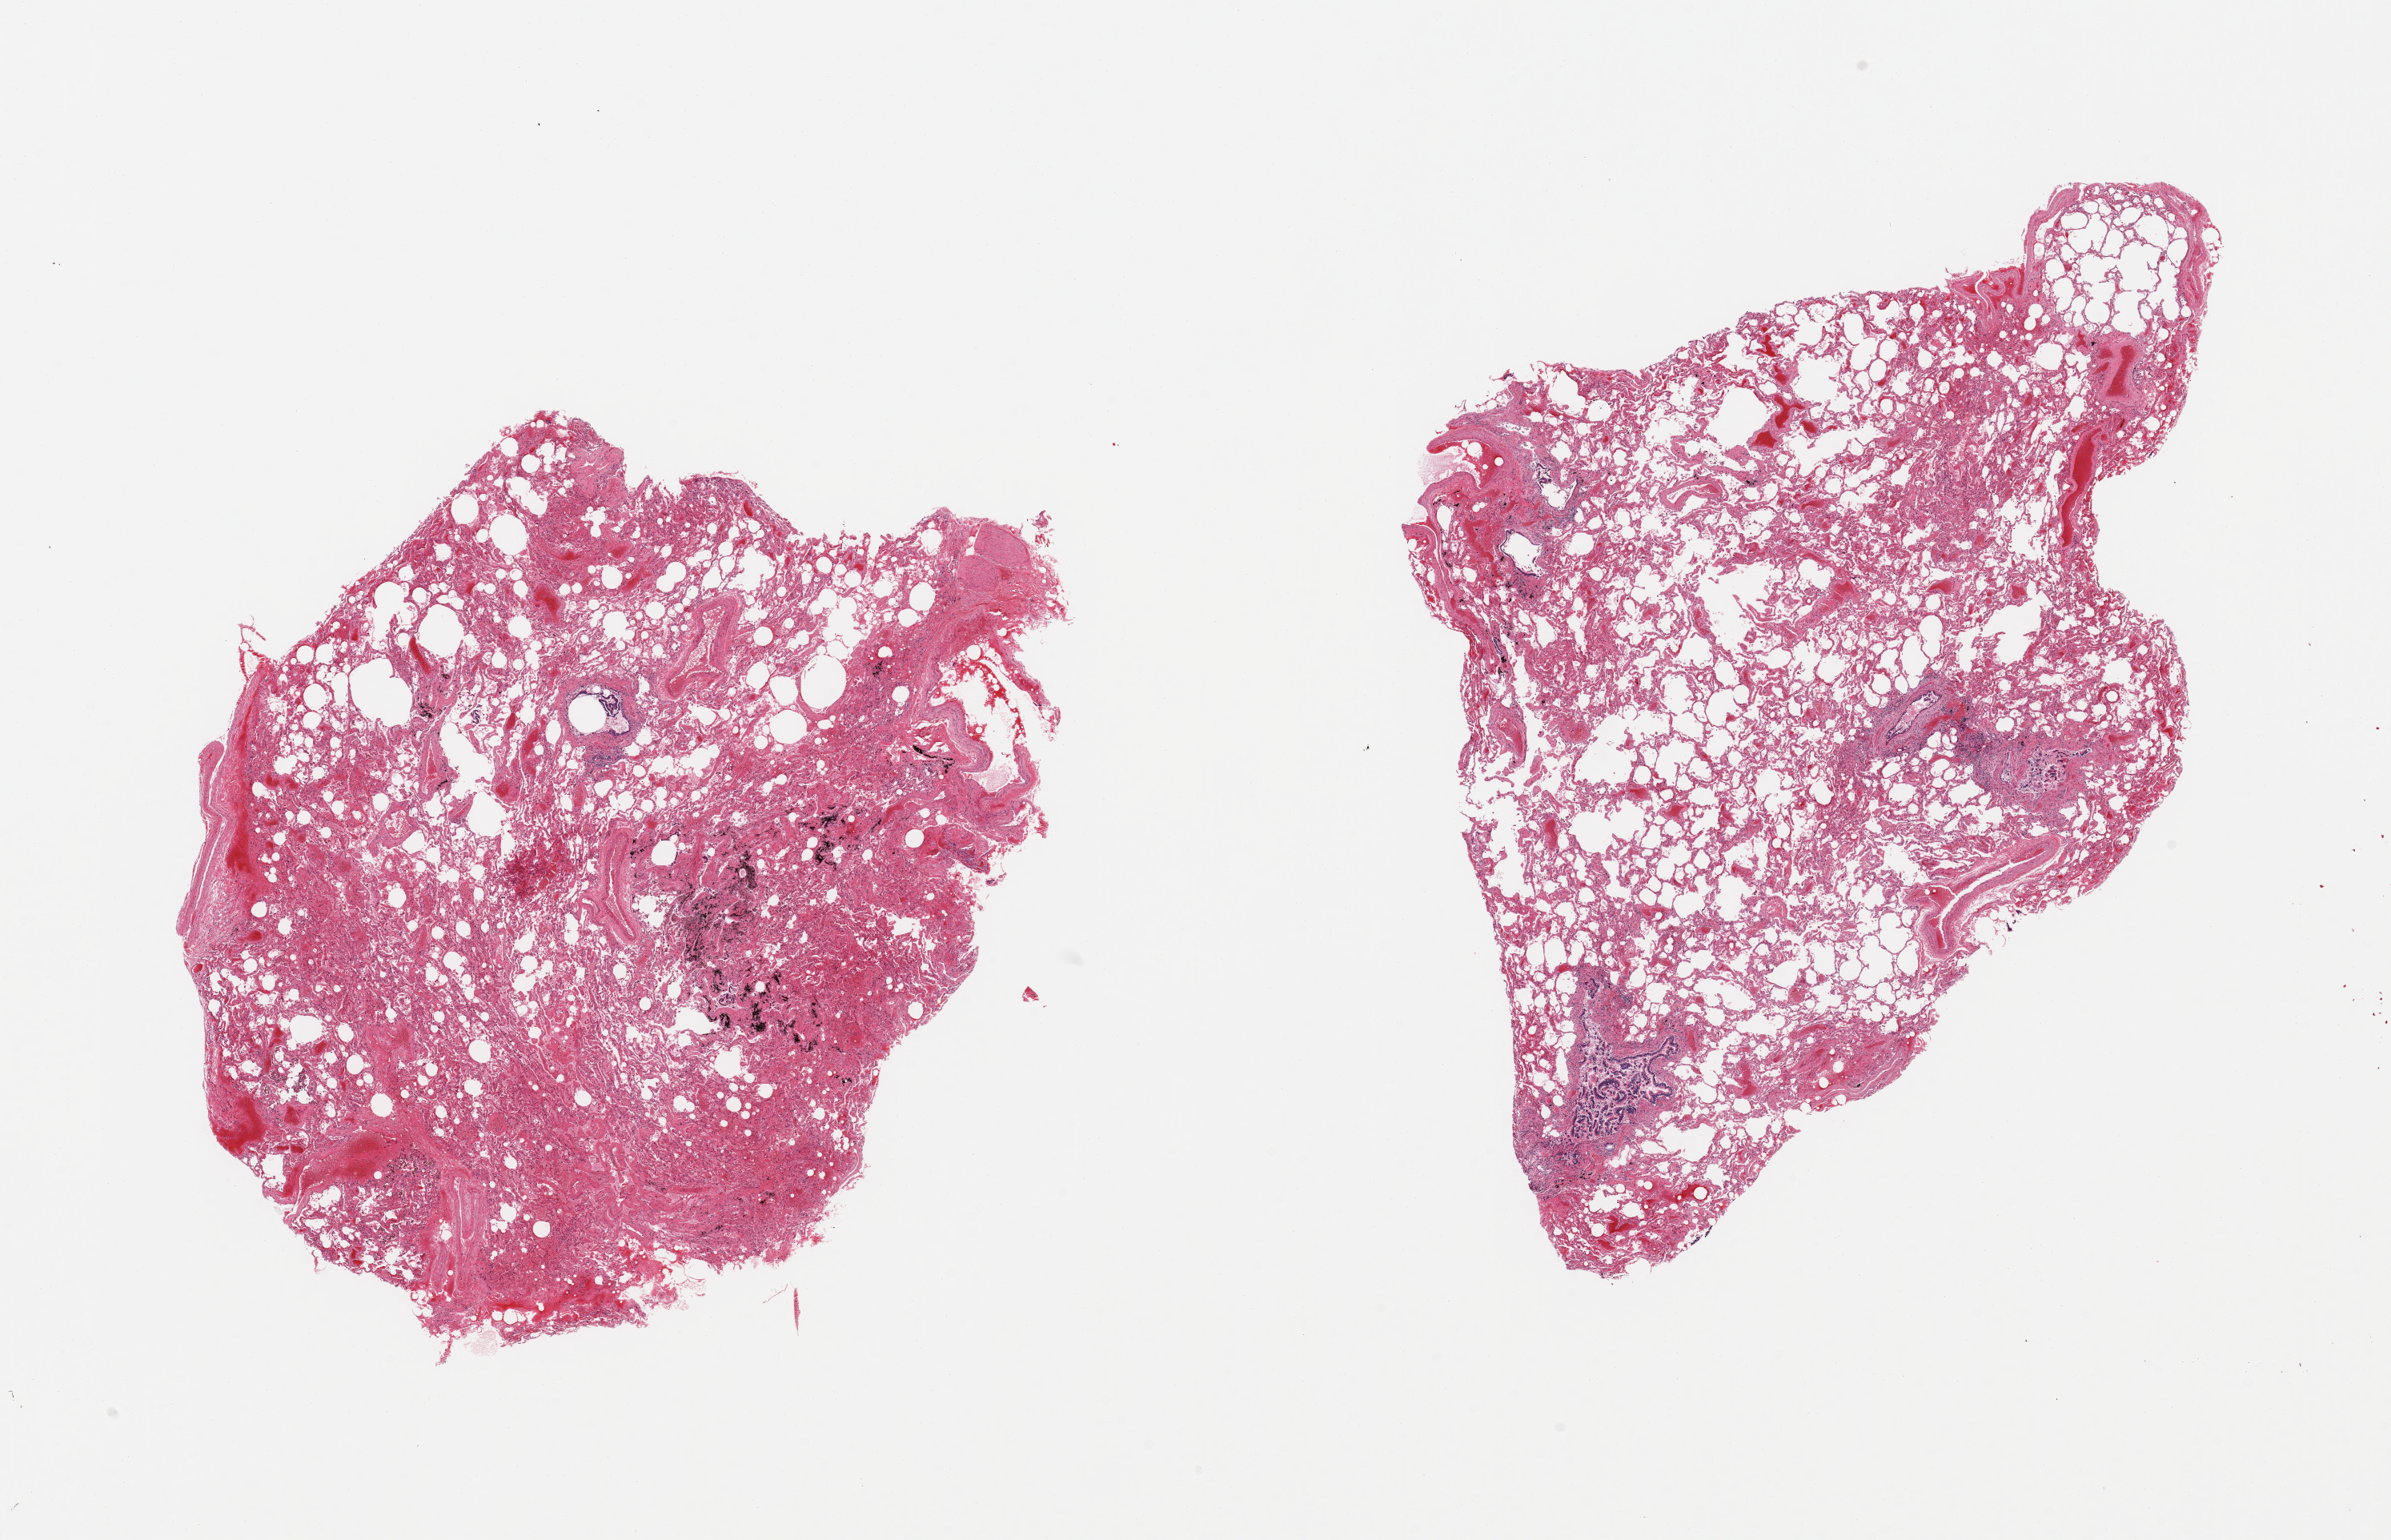
Digitized H&E-stained section — a low-resolution overview of the entire scanned area, about 23.6 x 15.2 mm (from a 20x scan), PAXgene-fixed paraffin-embedded (PFPE) section, sampled site (target tissue): lung, tissue donor sample.
Reviewer comment on this tissue sample: 2 pieces; some congestion, anthracotic pigment, some fibrosis and pigmented macrophages, widening of airspaces.